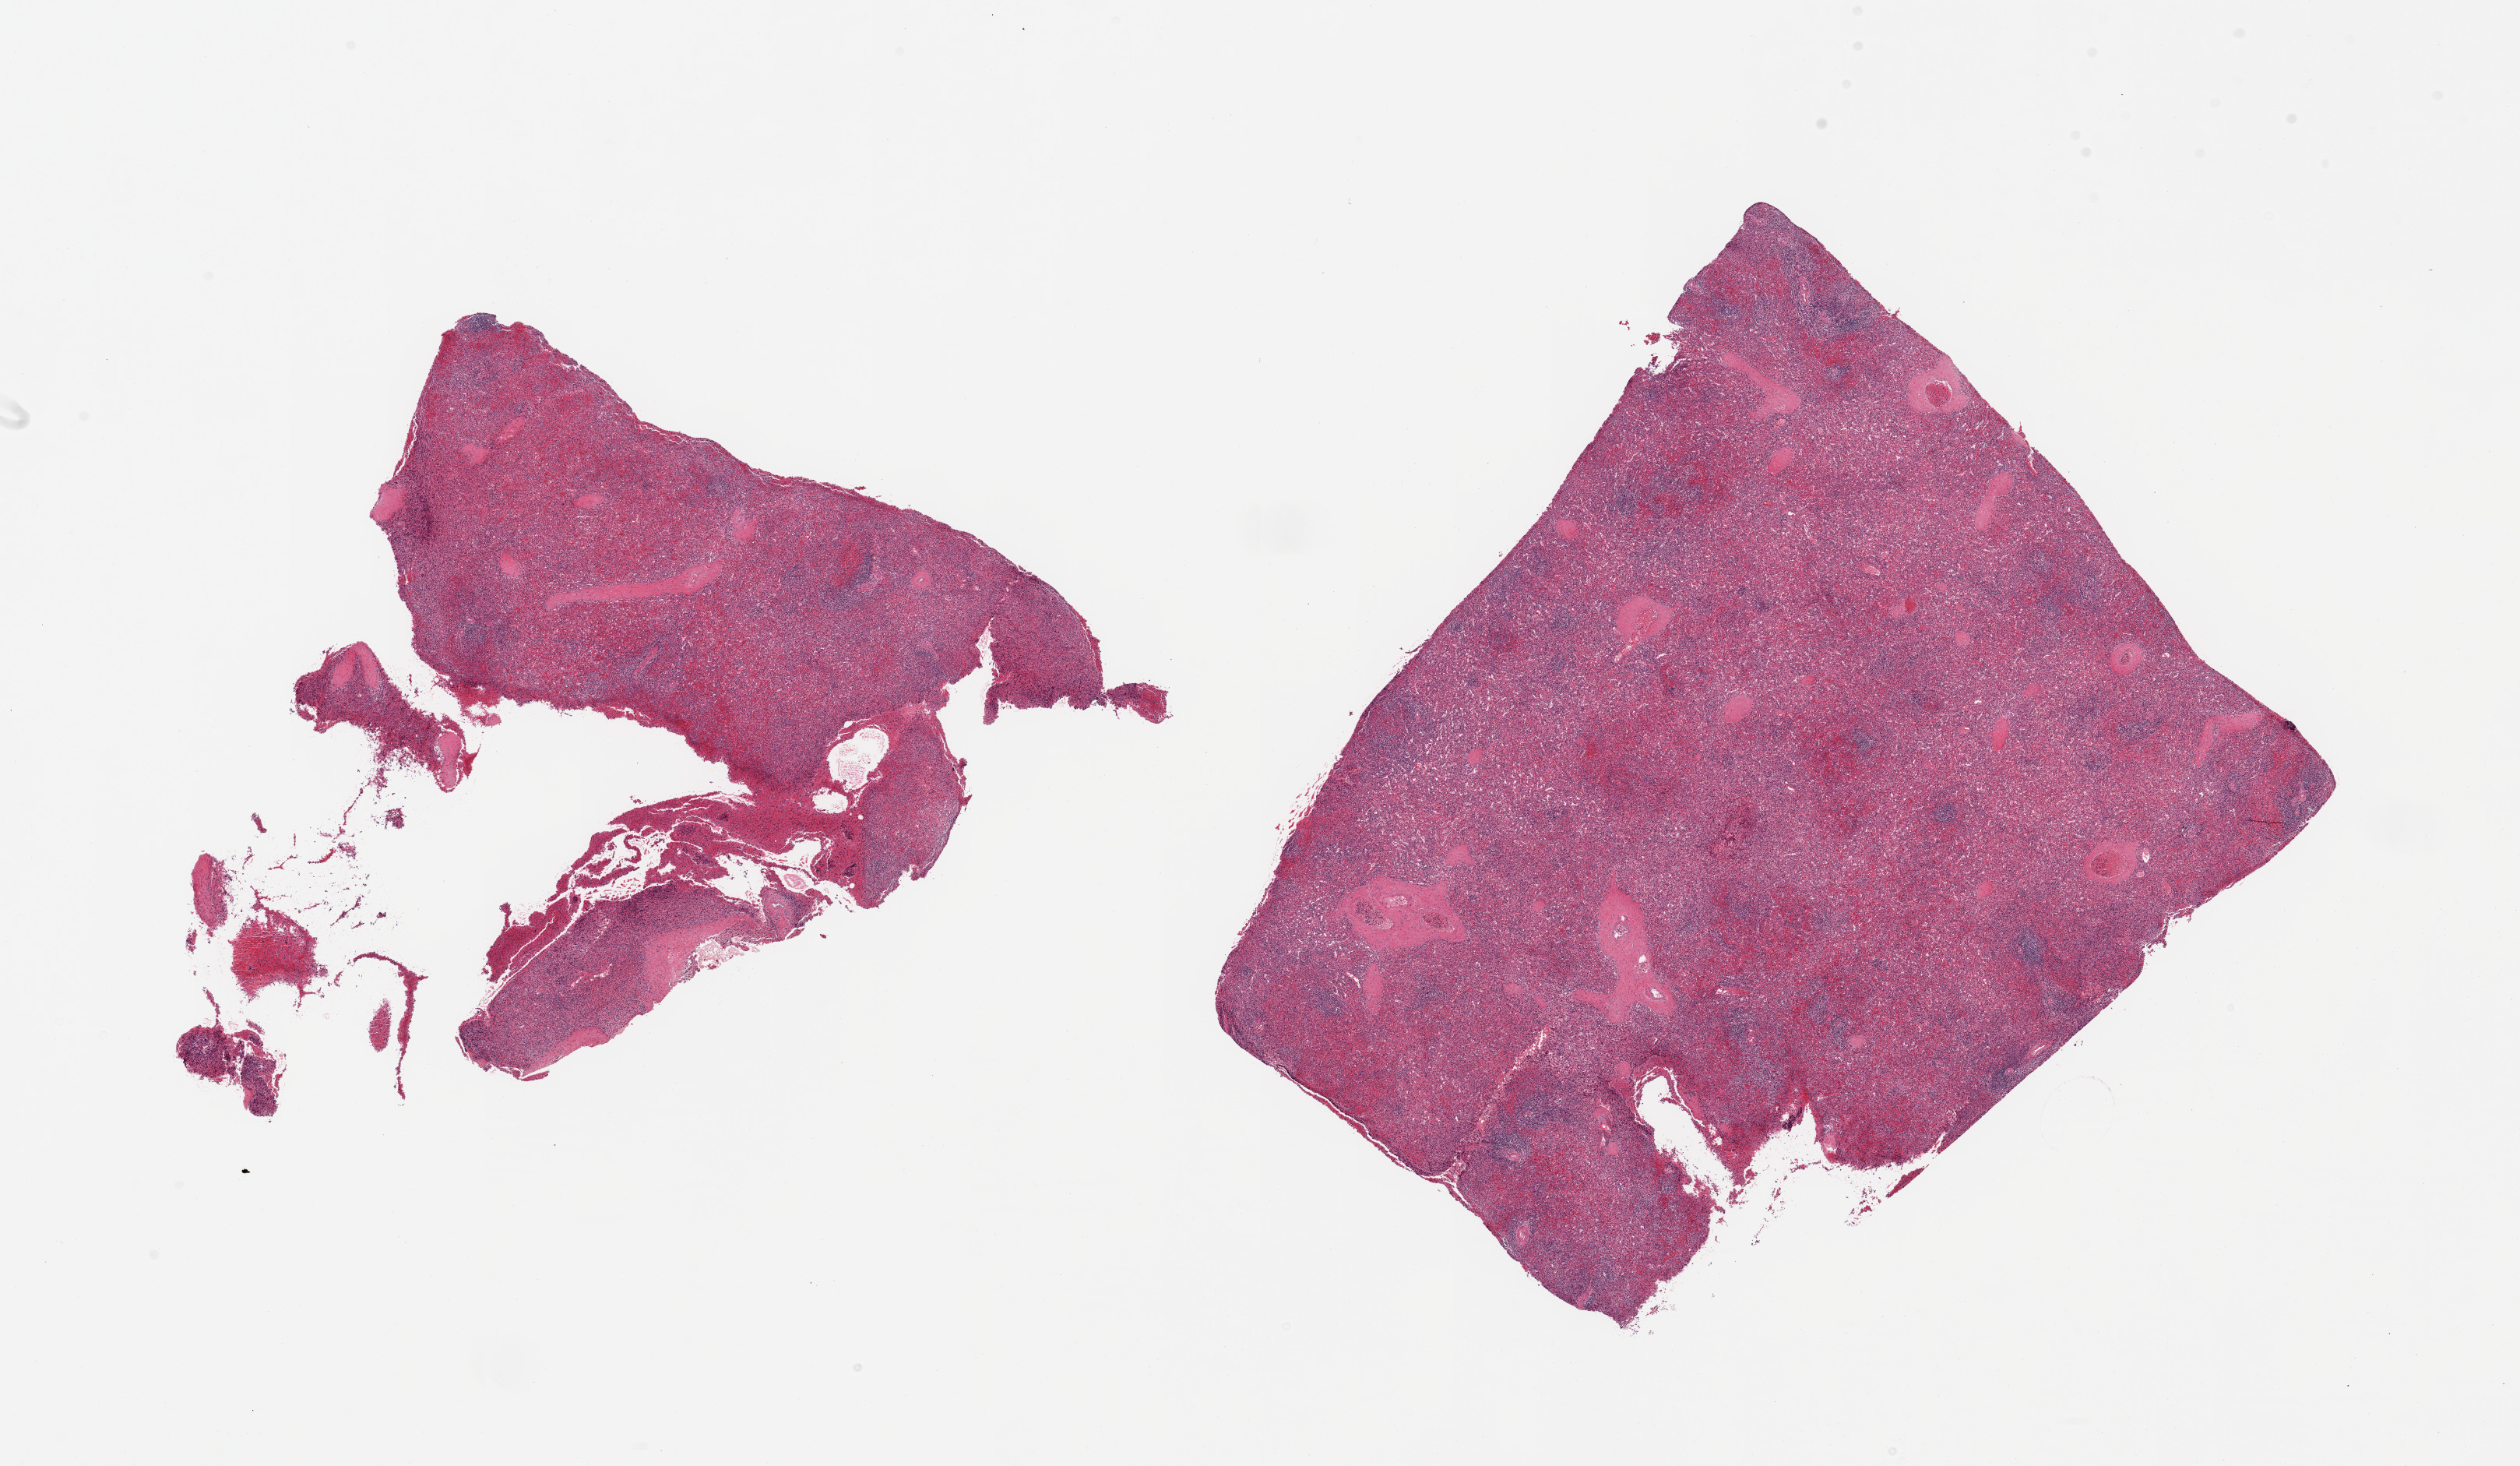
Digitized hematoxylin and eosin (H&E)-stained section — a low-resolution overview of the entire scanned area, about 25.6 x 14.9 mm, PAXgene-fixed, paraffin-embedded tissue, target tissue: spleen, tissue donor sample. Female donor.
Review note (as recorded): 2 pieces, spleen, depleted -appearing red pulp.